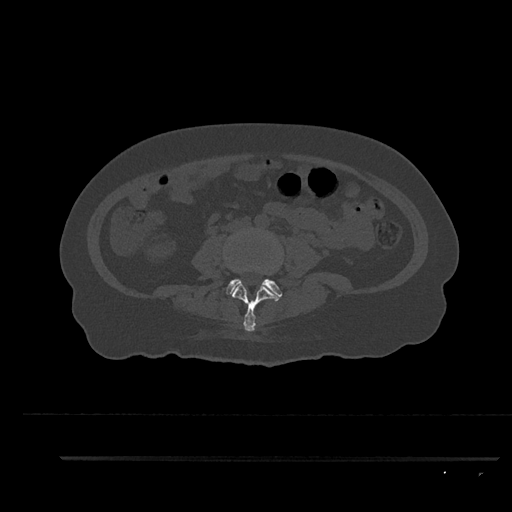
CT including the spine, one axial slice. Slice 54 of 797 in the series (ordered by position). Reconstruction kernel Br40s/3. 120 kVp. Bone window (W 1800 / L 400 HU). 512 × 512 image matrix, field of view 408 × 408 mm. Female patient, age 44 years. From the clinical record (not read from this slice): primary cancer: renal; vertebrae with lytic lesions (as recorded): L1.
Outlined on this slice (semi-automatically segmented with operator editing):
- L3 vertebra: bounding box [x1, y1, x2, y2] px = [232, 282, 282, 331]
- L4 vertebra: [225, 267, 282, 297]